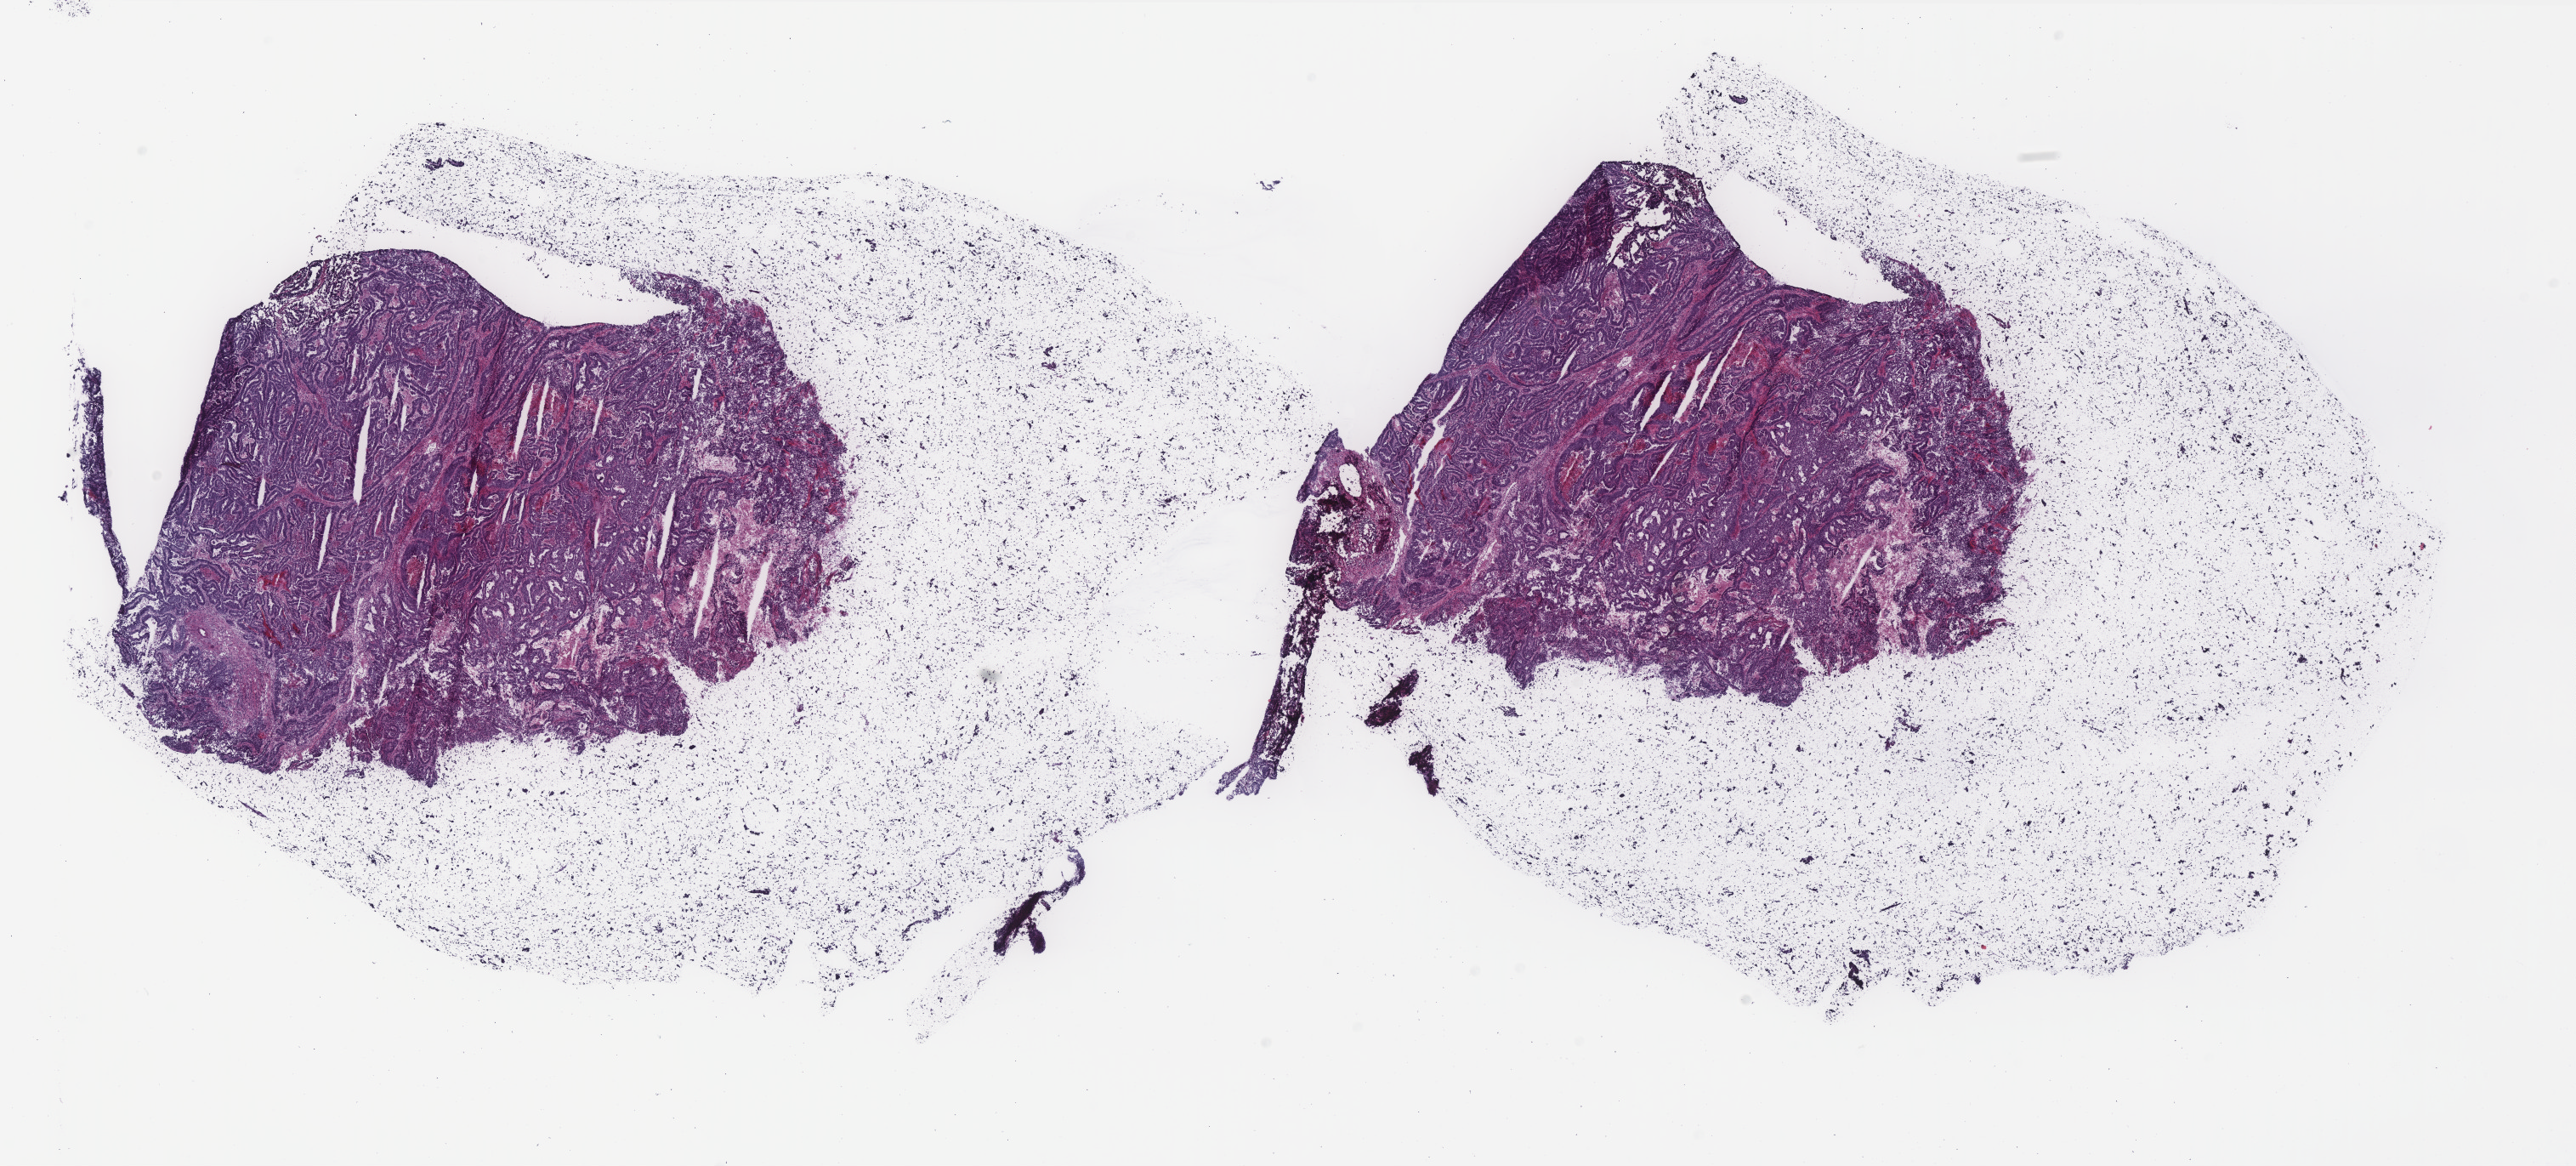
Hematoxylin and eosin (H&E) stained whole-slide image, low-resolution overview of the scanned area, about 24.3 x 11.0 mm (from a 40x scan); frozen section from the top of the tissue portion; sample: primary tumour, uterus. Patient: female, age at initial diagnosis 86 years. Histologic grade: G2 (moderately differentiated). Slide review estimates, as recorded: tumour cells 50%, tumour nuclei 70%, normal cells 20%, stromal cells 10%, necrosis 20%. Inflammatory infiltration, as recorded: lymphocyte infiltration 20%, monocyte infiltration 0%, neutrophil infiltration 20%.
- pathologic diagnosis: Endometrioid adenocarcinoma, NOS (endometrium)
- FIGO stage: II